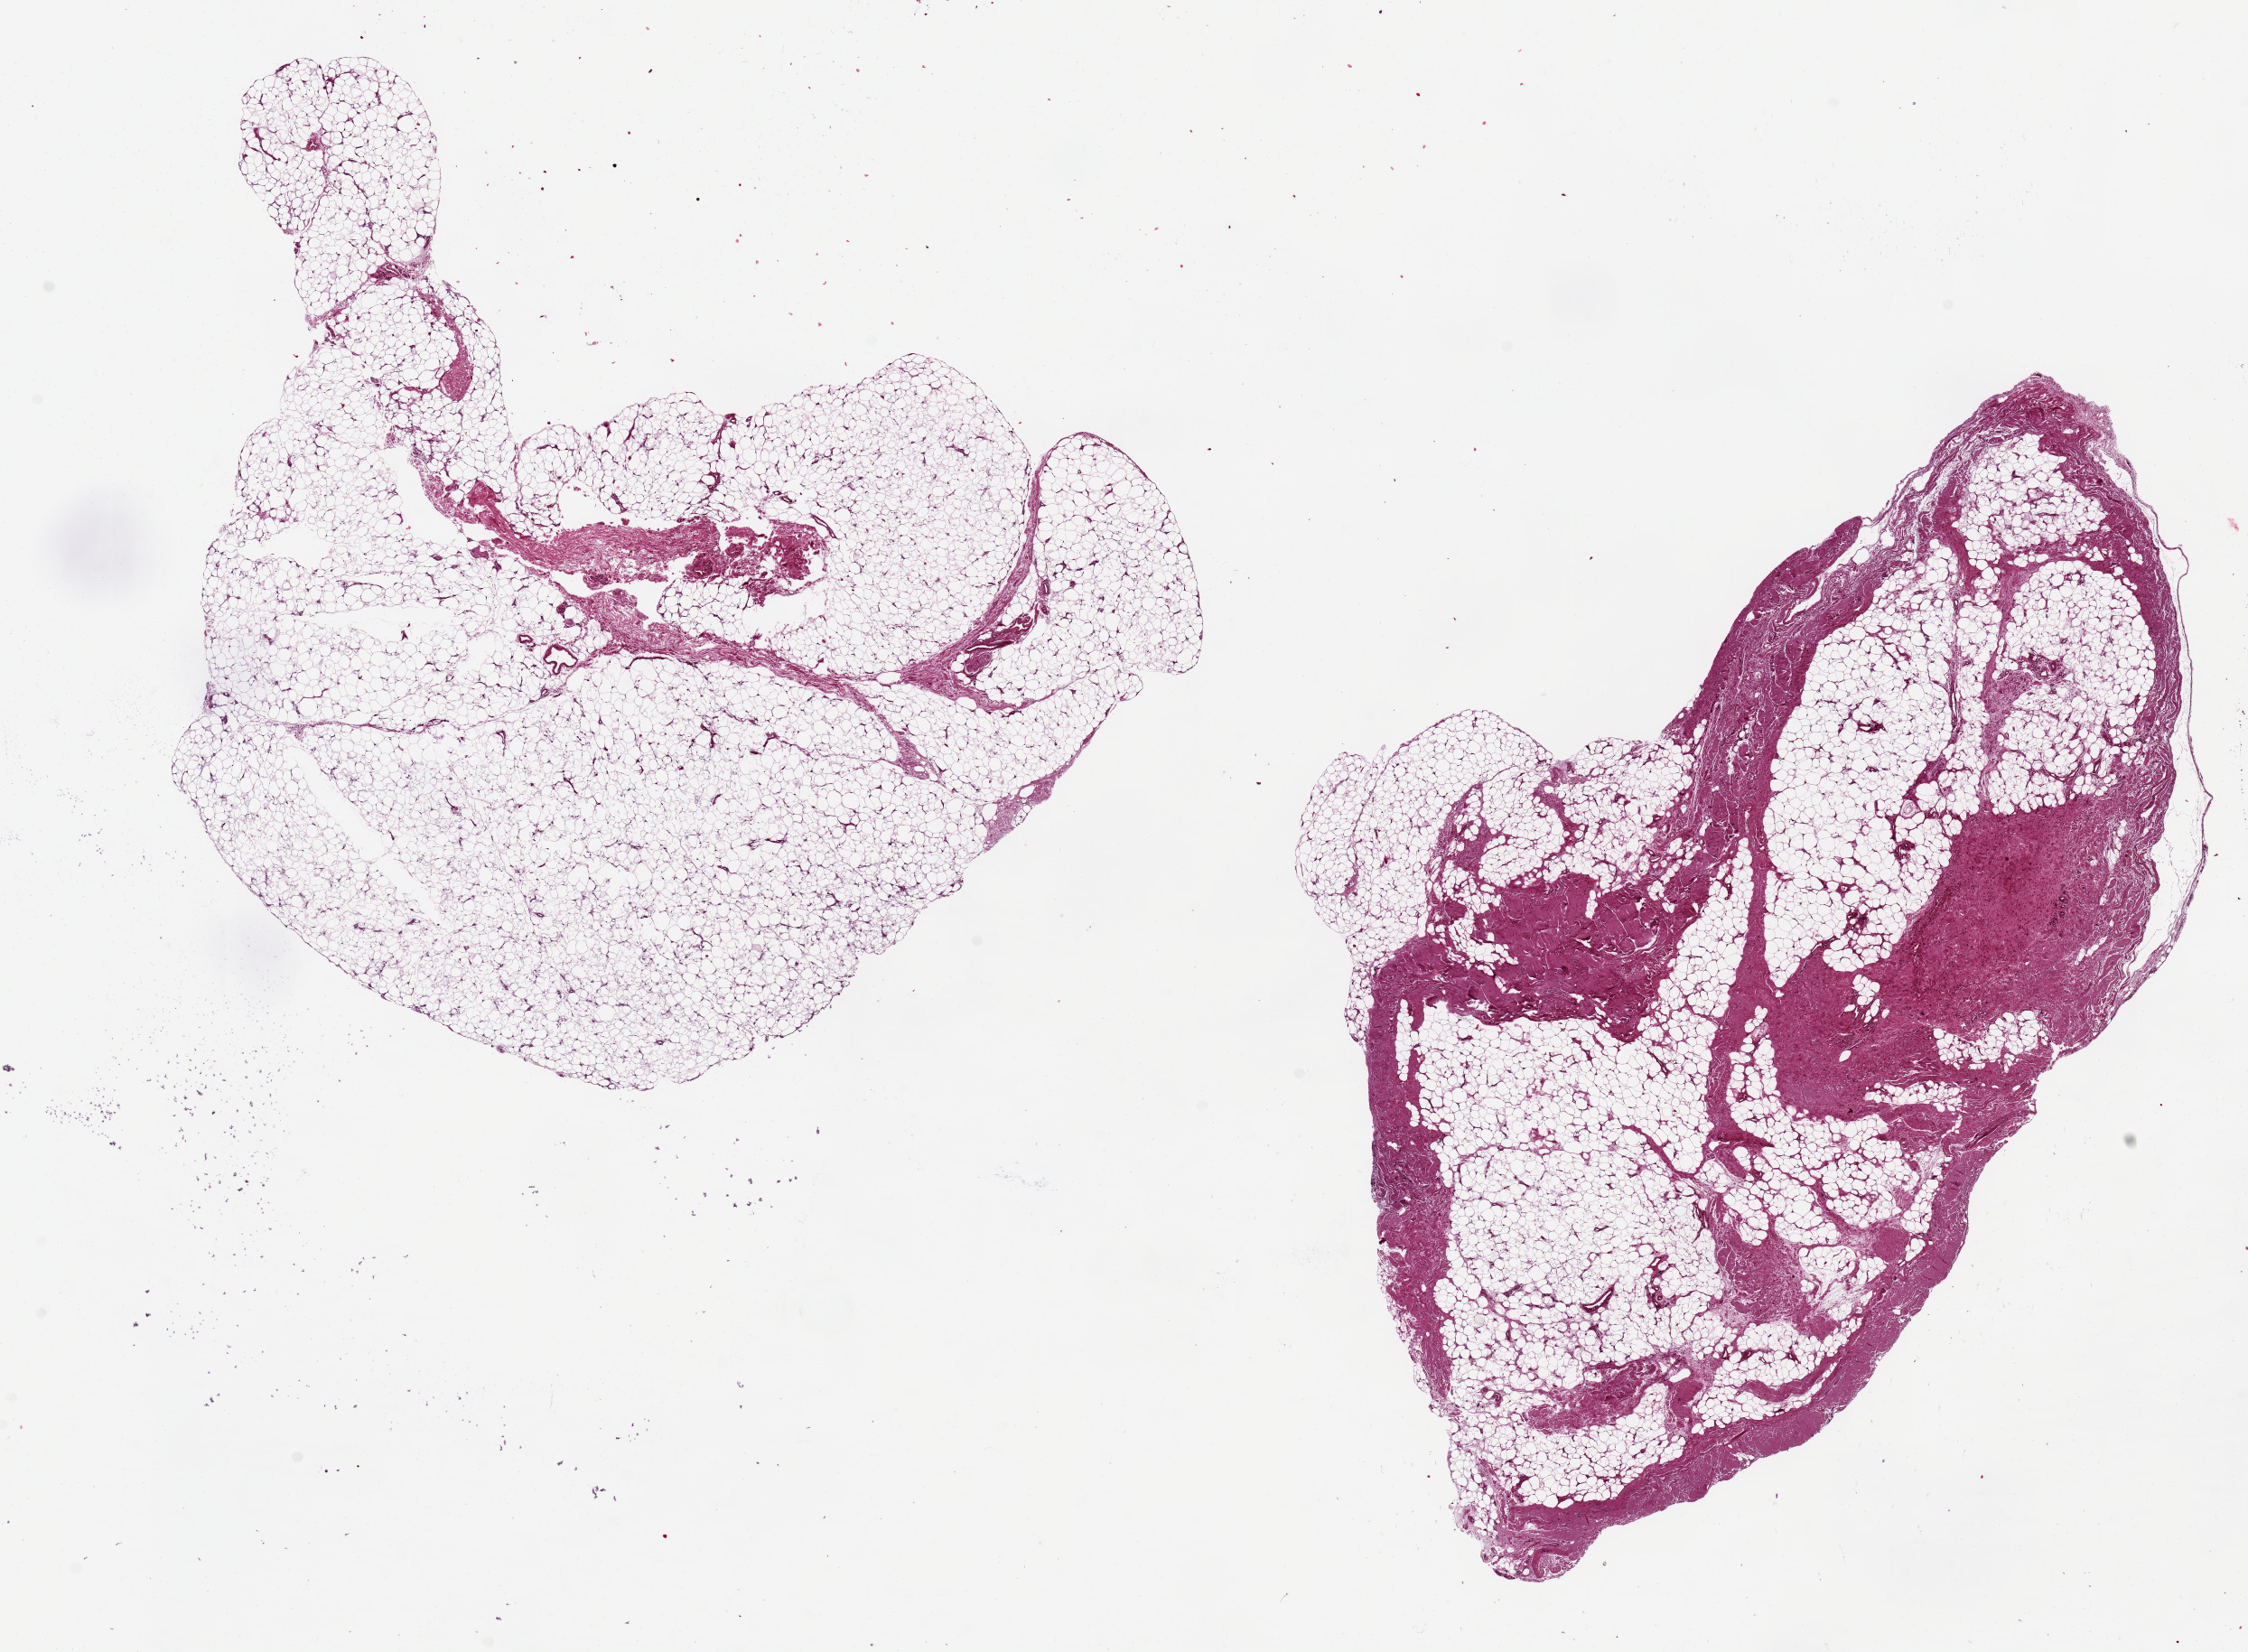
Haematoxylin and eosin whole-slide image — whole scanned area (about 19.7 x 14.5 mm) shown as a low-resolution overview; PAXgene-fixed paraffin-embedded (PFPE) section; target tissue: adipose tissue; tissue donor sample. Male donor.
* pathologist's review note for this sample: 2 ~9x6mm aliquots, one with ~40% fibrous (?scar) tissue